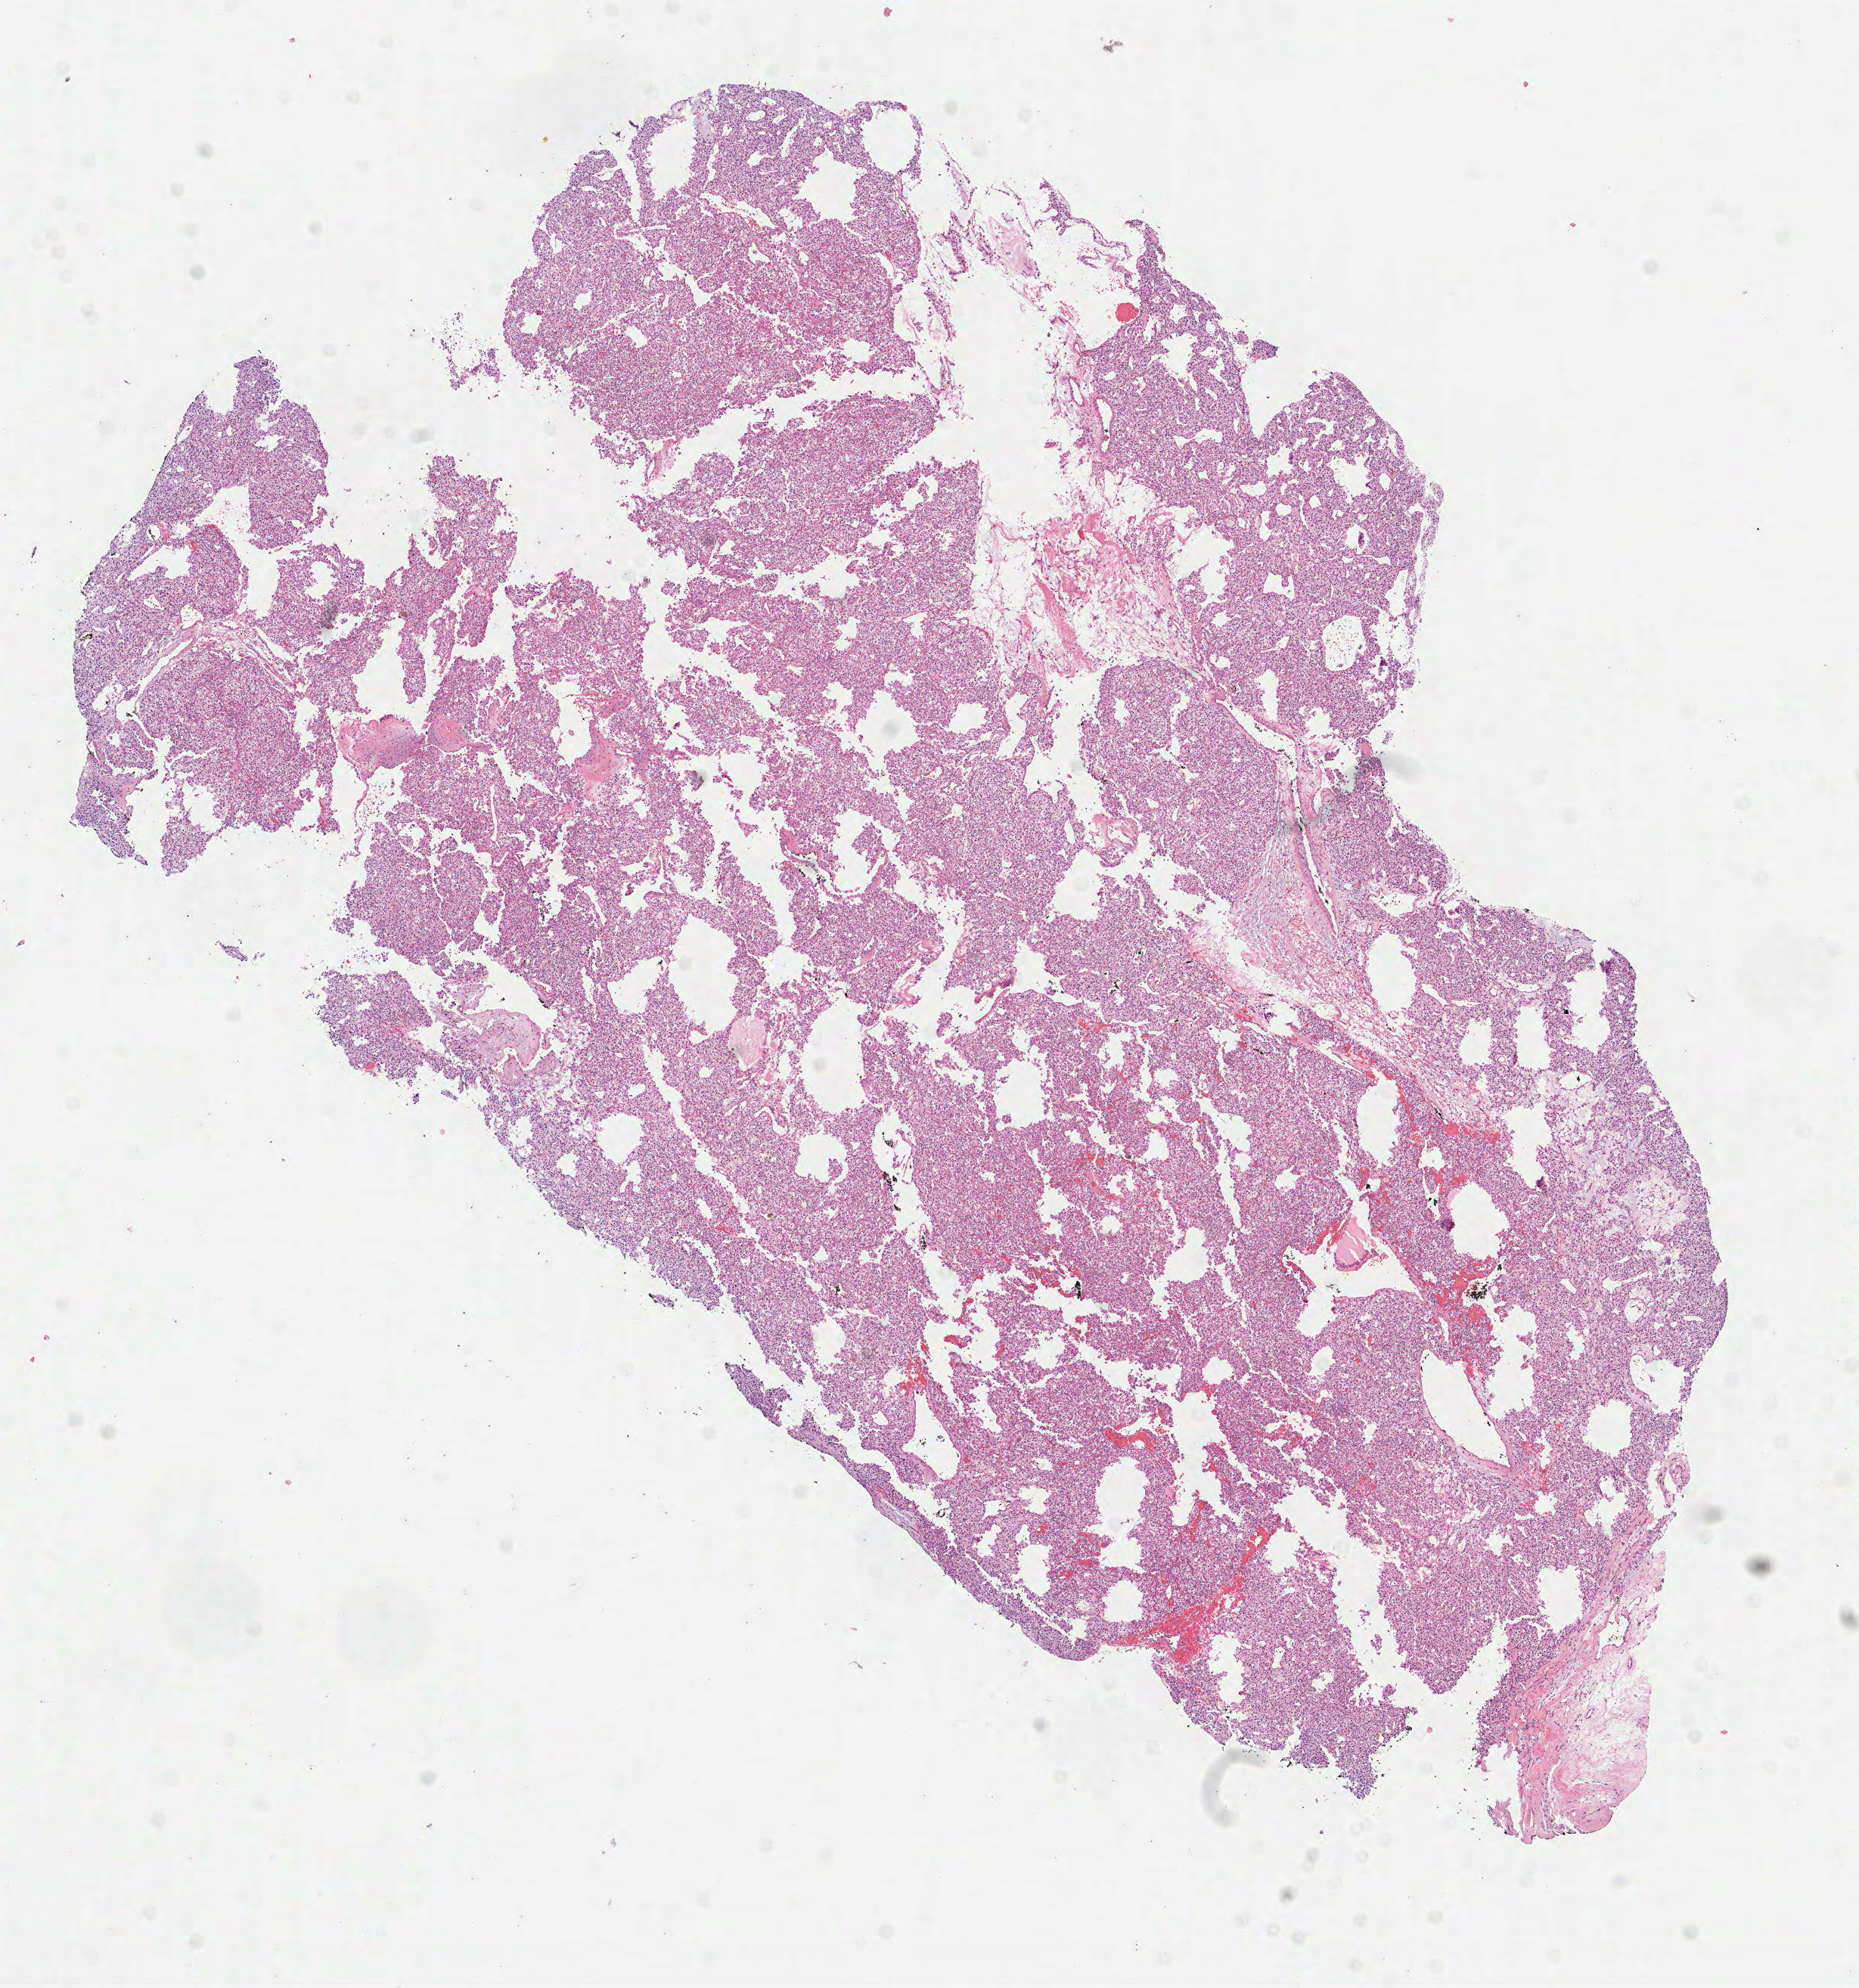
Digitized Hematoxylin and eosin (H&E) stained tissue section (whole slide), whole scanned area (about 9.9 x 10.6 mm, slide scanned at 40x) shown as a low-resolution overview, FFPE section, kidney, primary tumour sample. Male patient; age at initial diagnosis 64 years. Histologic grade: G2 (moderately differentiated).
AJCC pathologic stage: III. Histologic diagnosis: Clear cell adenocarcinoma, NOS. Laterality: left.